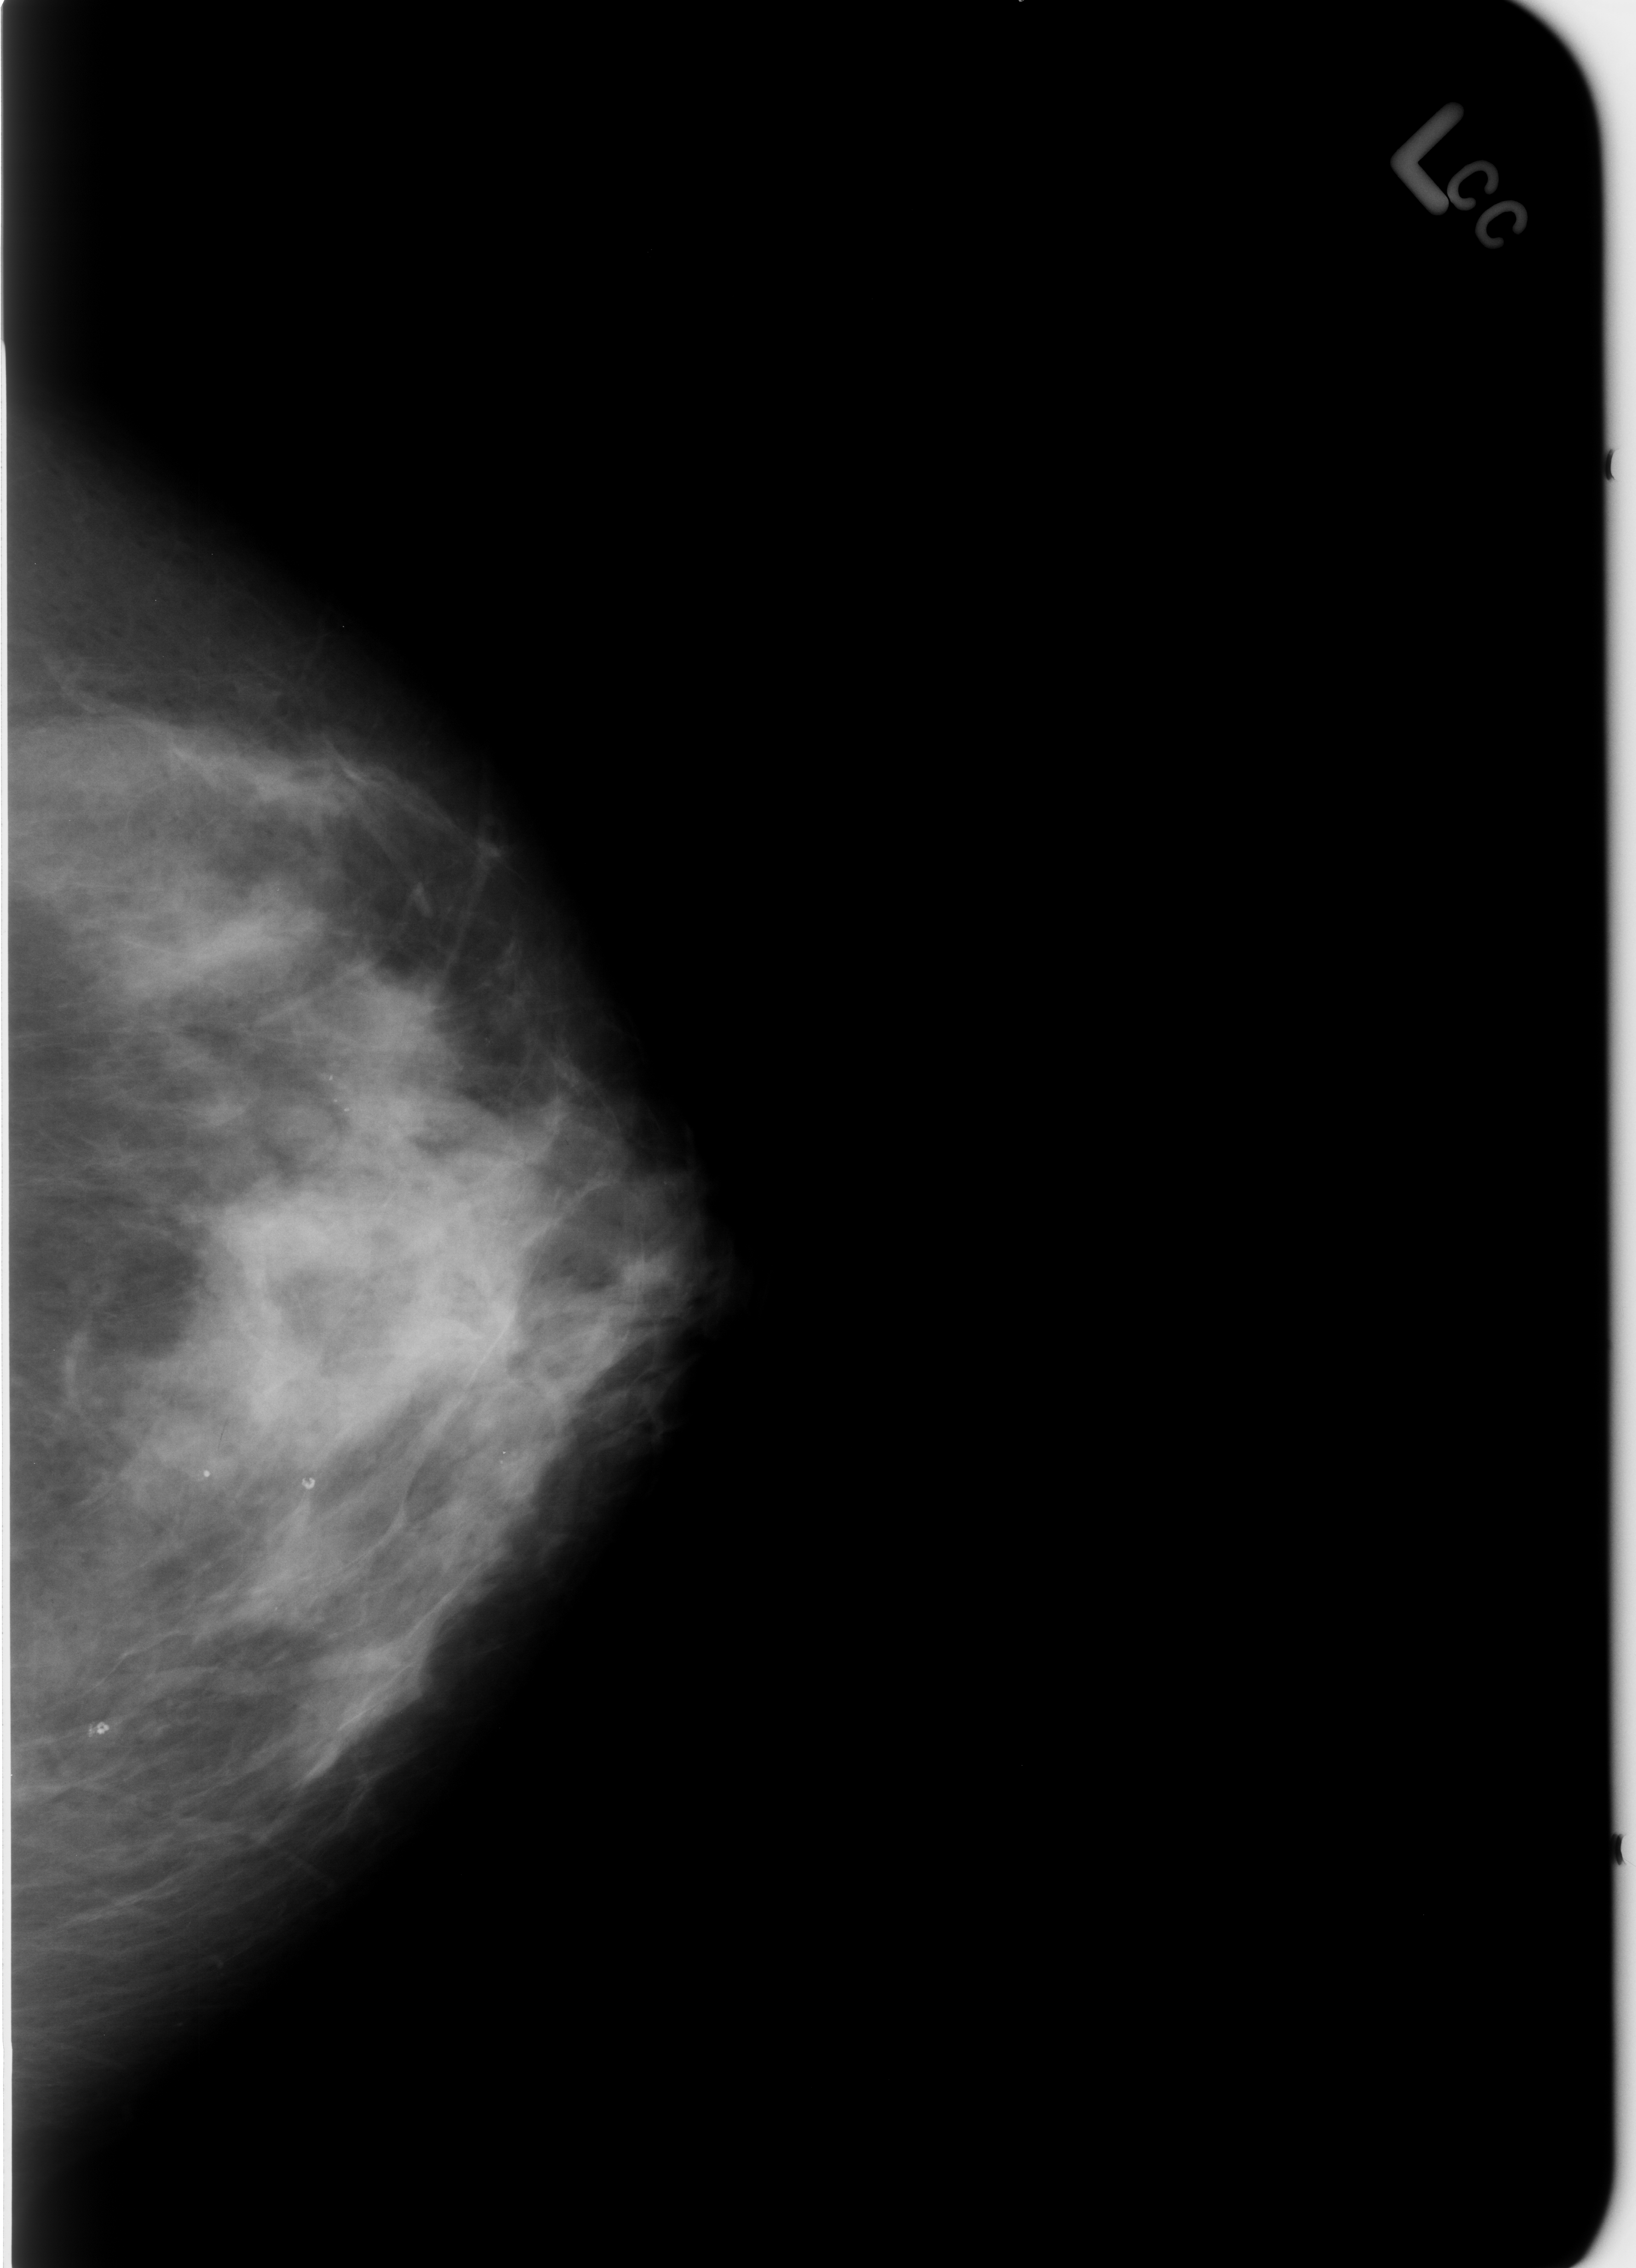
Digitized screen-film mammogram, left breast, CC view, breast composition: heterogeneously dense (BI-RADS density category 3 of 4).
Radiologist-marked abnormalities on this image: Finding 1 of 3: calcifications, morphology round and regular / lucent center; BI-RADS assessment category 2; subtlety rating 5 on a 1 (subtle) to 5 (obvious) scale; benign; no additional work-up was recommended (benign without callback). Finding 2 of 3: calcifications, morphology round and regular / lucent center; BI-RADS assessment category 2; subtlety rating 5 on a 1 (subtle) to 5 (obvious) scale; benign; no additional work-up was recommended (benign without callback). Finding 3 of 3: calcifications, morphology round and regular / lucent center; BI-RADS assessment category 2; subtlety rating 5 on a 1 (subtle) to 5 (obvious) scale; benign without callback (not worked up further).